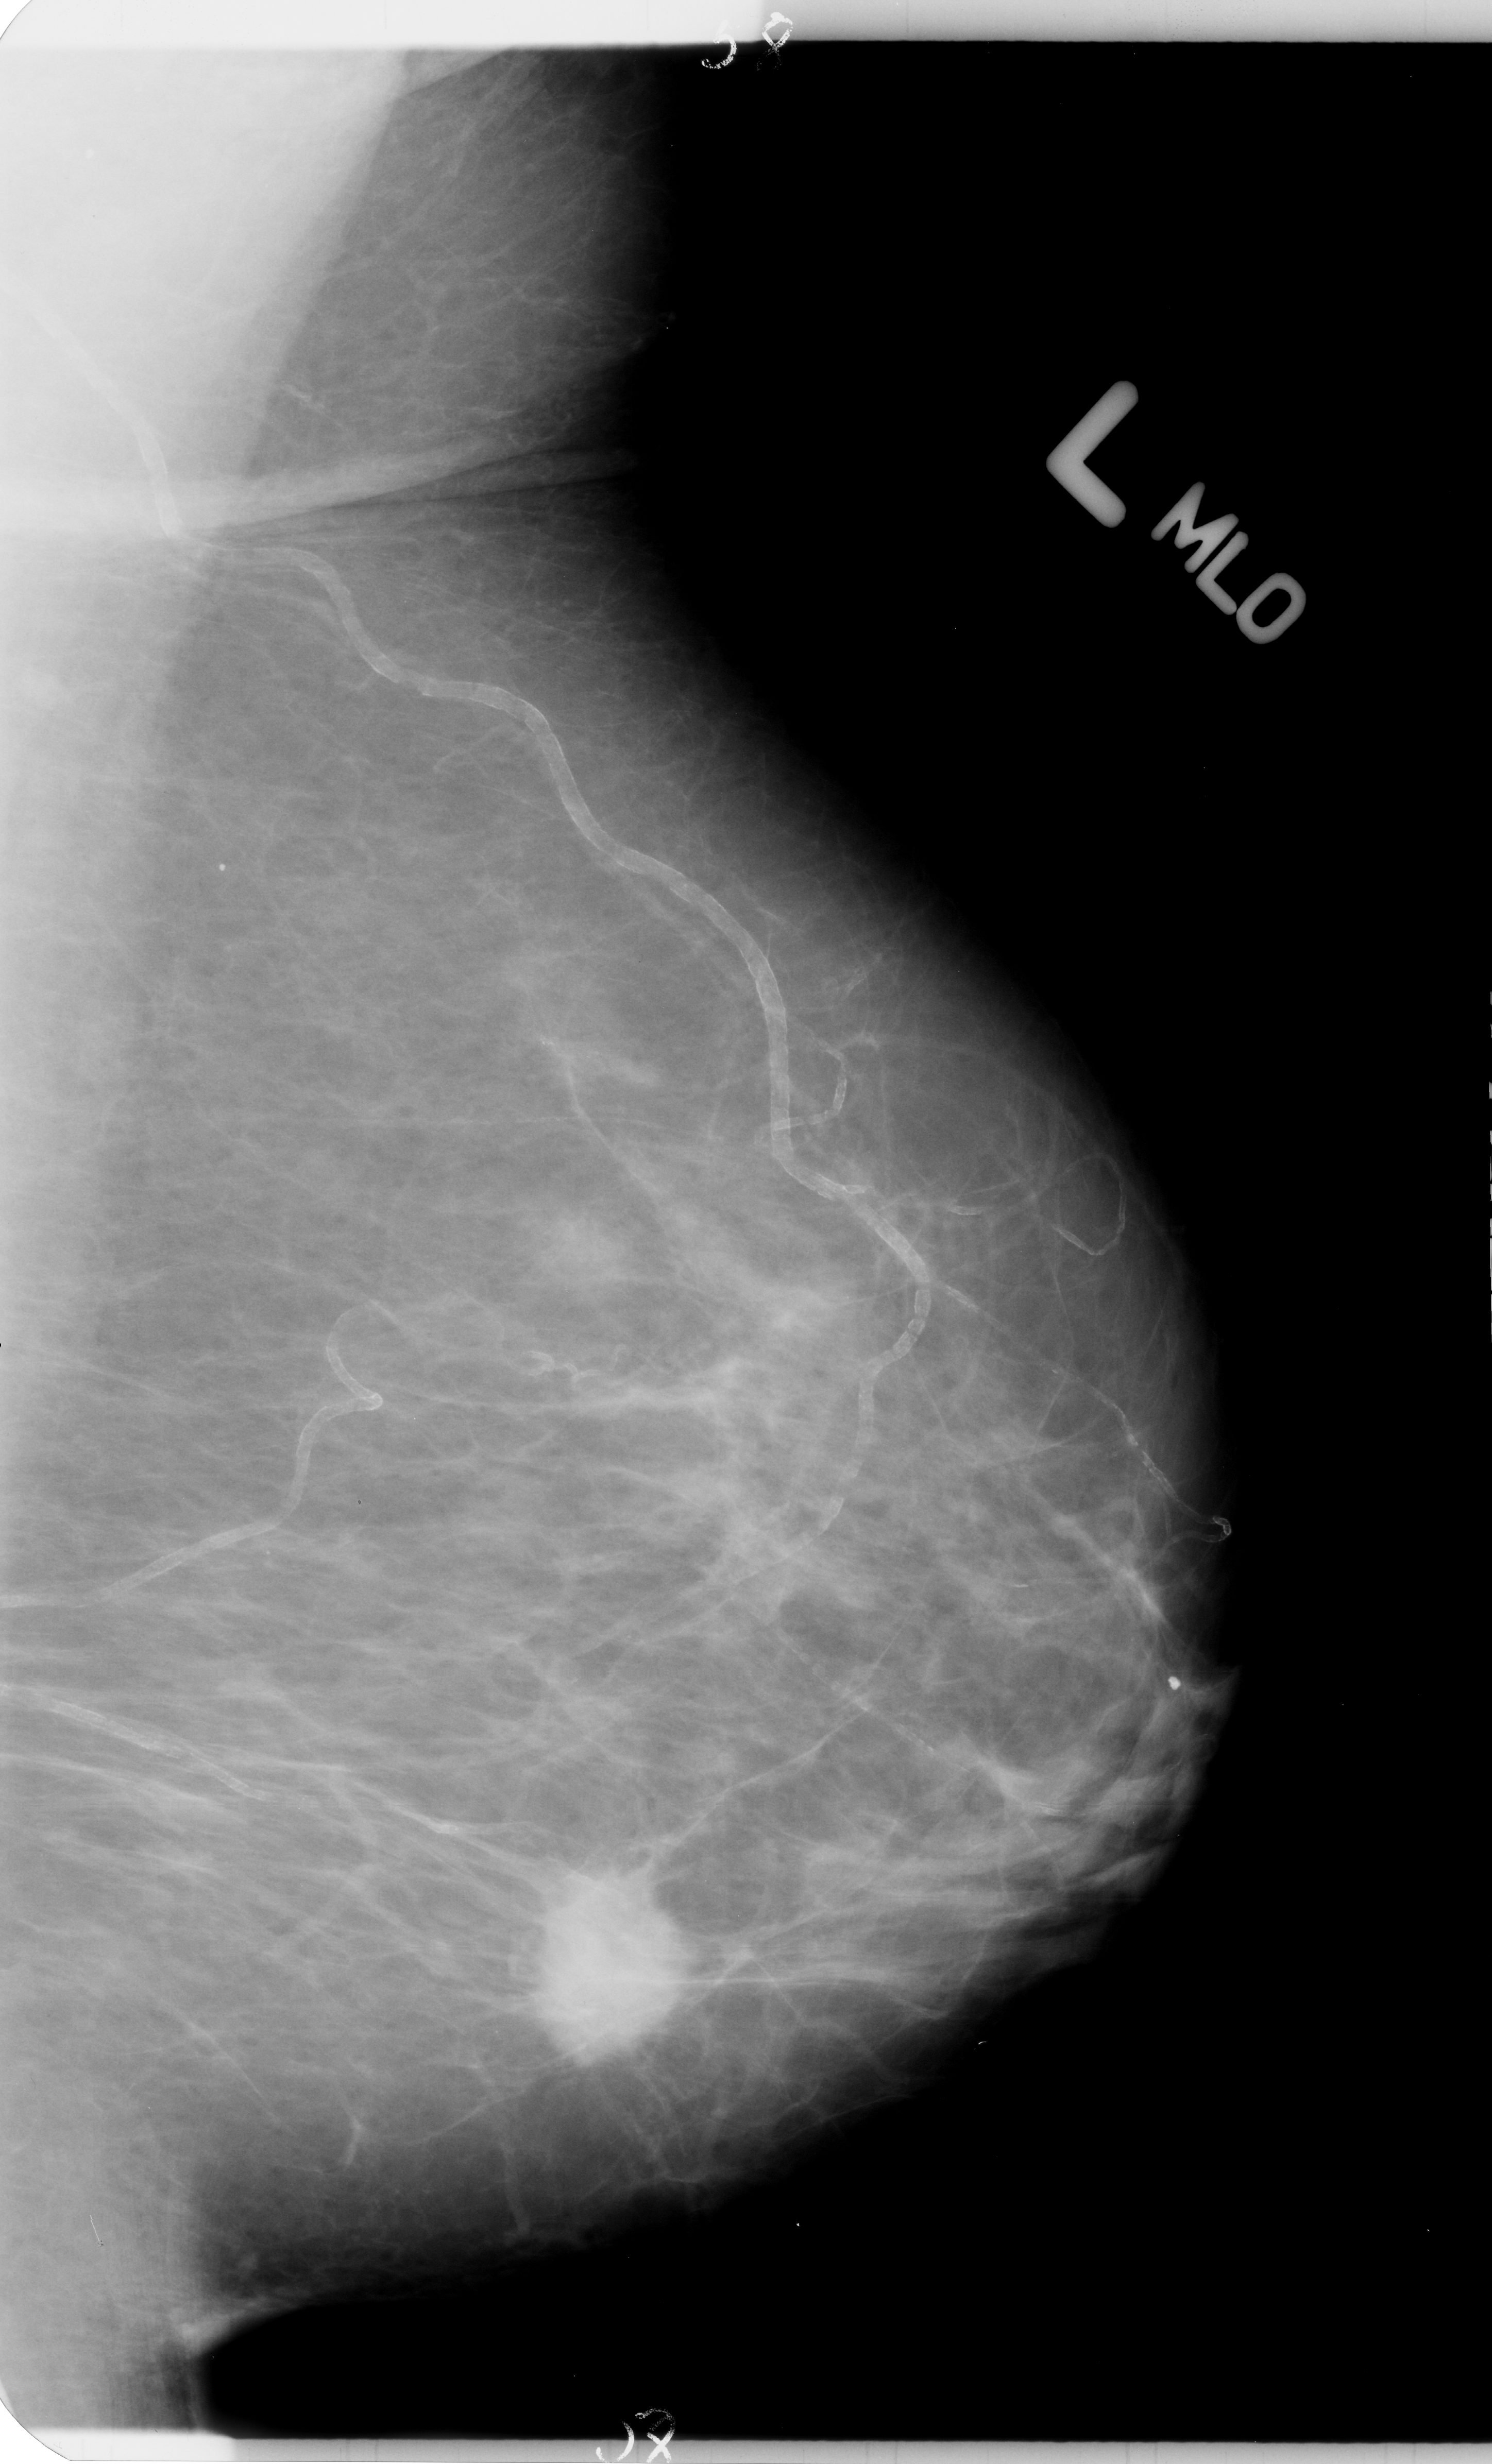
Scanned film-screen mammogram; left breast; mediolateral oblique (MLO) view; BI-RADS breast density category 2 (scale 1–4); 1492 × 2464 image matrix.
Marked abnormalities (boxes around the expert regions of interest):
- mass, shape round, margins spiculated; BI-RADS assessment category 4; pathology result (as recorded, not read from the image): malignant: bounding box (x1, y1, x2, y2) in pixels: (526, 1892, 679, 2046)